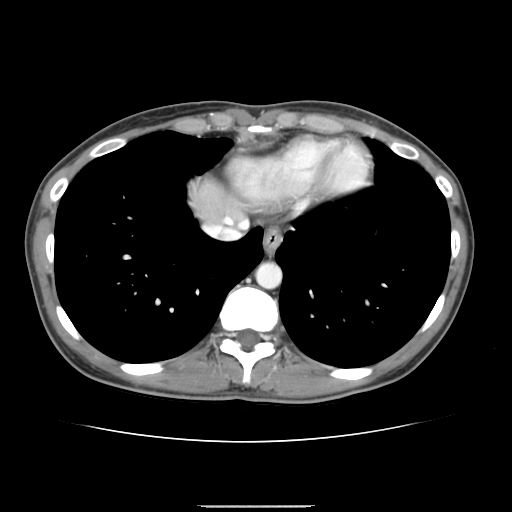
Contrast-enhanced abdominal CT, one axial slice. Position 137 of 150 along the scan axis. 120 kVp. Intravenous contrast given. Soft-tissue window (W 400 / L 40 HU). 2.5 mm slice thickness. 512 × 512 image matrix, field of view 324 × 324 mm. Female patient, age 32 years. From the clinical record (not read from this slice): diagnosis: colorectal cancer liver metastases, imaged before liver resection; multiple liver metastases: yes; largest metastasis: 0.7 cm; disease in both lobes: no.
Annotated regions visible in this slice (manually delineated by an expert):
- hepatic veins: bounding box (x1, y1, x2, y2) in pixels: (219, 234, 223, 237)
- liver: (195, 184, 240, 225)
- planned liver remnant (the part of the liver to remain after resection): (195, 184, 239, 225)
- portal vein (with intrahepatic branches): (225, 217, 232, 224)